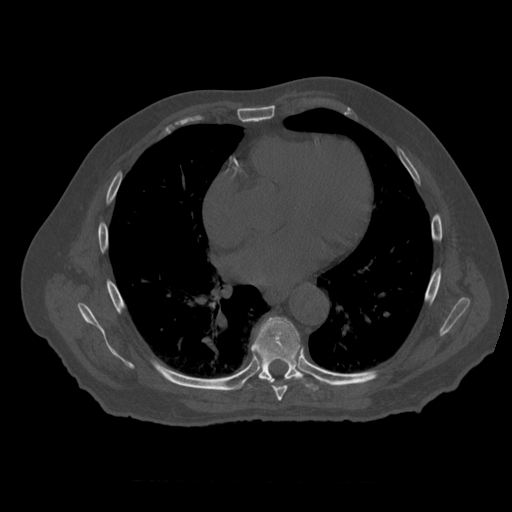
CT including the spine, one axial slice. Position 350 of 399 along the scan axis. Reconstruction kernel STANDARD. 120 kVp. Bone window (W 1800 / L 400 HU). 1.25 mm slice thickness. 512 × 512 image matrix, field of view 407 × 407 mm. Patient age 73 years. From the clinical record (not read from this slice): primary cancer: prostate.
Annotated regions visible in this slice (semi-automatically segmented with operator editing):
- T7 vertebra: box from (x=272, y=376) to (x=304, y=401) px
- T8 vertebra: (x=248, y=317)–(x=319, y=391)